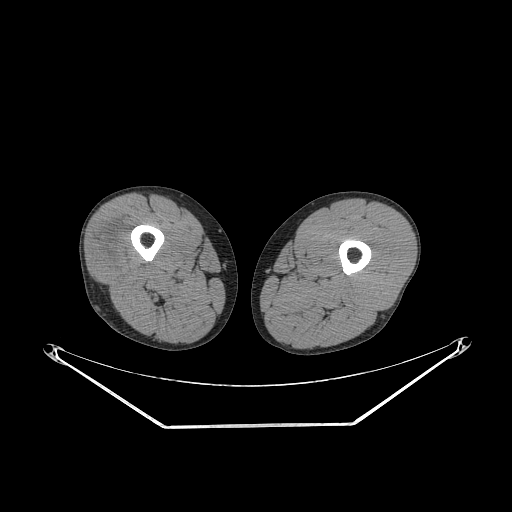
CT of an extremity soft-tissue mass (from a PET/CT study), one axial slice; reconstruction kernel STANDARD; 140 kVp; soft-tissue window (W 400 / L 40 HU); 512 × 512 image matrix. Male patient. Case-level facts recorded for this patient, not image findings: histological type: poorly differentiated synovial sarcoma; grade: high; site of the primary tumour: right buttock.
Annotated regions visible in this slice (expert contour drawn on MRI and transferred to this co-registered scan by the dataset authors):
- gross tumour volume including surrounding oedema: bounding box [x1, y1, x2, y2] px = [98, 233, 136, 273]